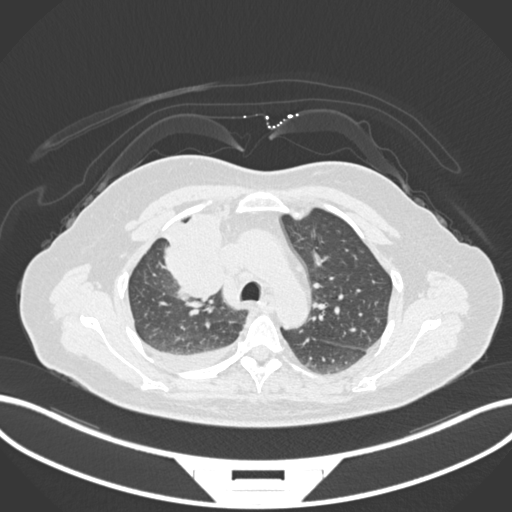
Chest CT, one axial slice; reconstruction kernel B30f; 120 kVp; lung window (W 1500 / L -600 HU); 1 mm slice thickness; 512 × 512 image matrix, field of view 400 × 400 mm. Female patient, age 52 years. From the clinical record (not read from this slice): clinical TNM (as recorded): T3 N1 M1.
Structures marked on this image (bounding box drawn by a radiologist):
- lung tumour (recorded histology: adenocarcinoma): bounding box (x1, y1, x2, y2) in pixels: (156, 209, 228, 310)